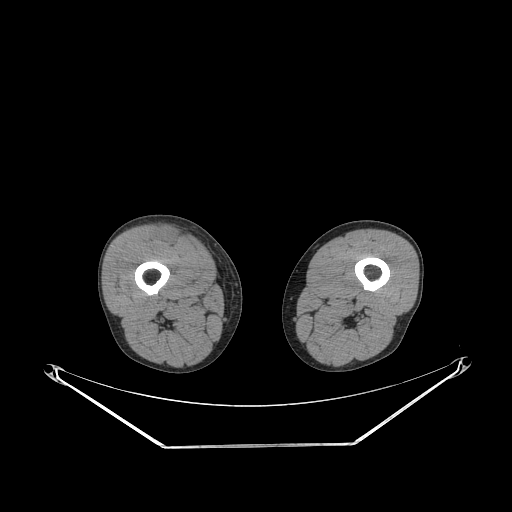
CT of an extremity soft-tissue mass (from a PET/CT study), one axial slice; position 231 of 311 along the scan axis; soft-tissue window (W 400 / L 40 HU); 512 × 512 image matrix. Male patient. Case-level facts recorded for this patient, not image findings: histological type: pleiomorphic leiomyosarcoma; grade: intermediate; site of the primary tumour: right thigh.
Outlined on this slice (expert contour drawn on MRI and transferred to this co-registered scan by the dataset authors):
- gross tumour volume including surrounding oedema: box from (x=157, y=228) to (x=182, y=245) px